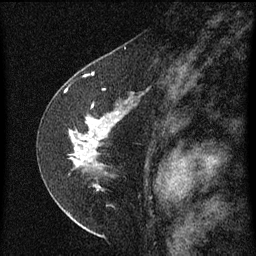
Breast MRI (dynamic contrast-enhanced), one sagittal slice. Position 37 of 60 along the scan axis. Dynamic contrast-enhanced series, image 2 of 3 at this slice position (ordered by acquisition). 1.5 T. TE 4.2 ms, TR 8 ms. 2 mm slice thickness. 256 × 256 image matrix, field of view 180 × 180 mm. Female patient, age 47 years.
Outlined on this slice (semi-automatically segmented with operator editing):
- analysis volume of interest (the breast-tissue region the enhancement analysis was run in; not a lesion): box from (x=44, y=84) to (x=141, y=199) px
- tumour enhancement mask (voxels above the 70 % enhancement threshold inside the analysis volume of interest): (x=72, y=112)–(x=119, y=161)